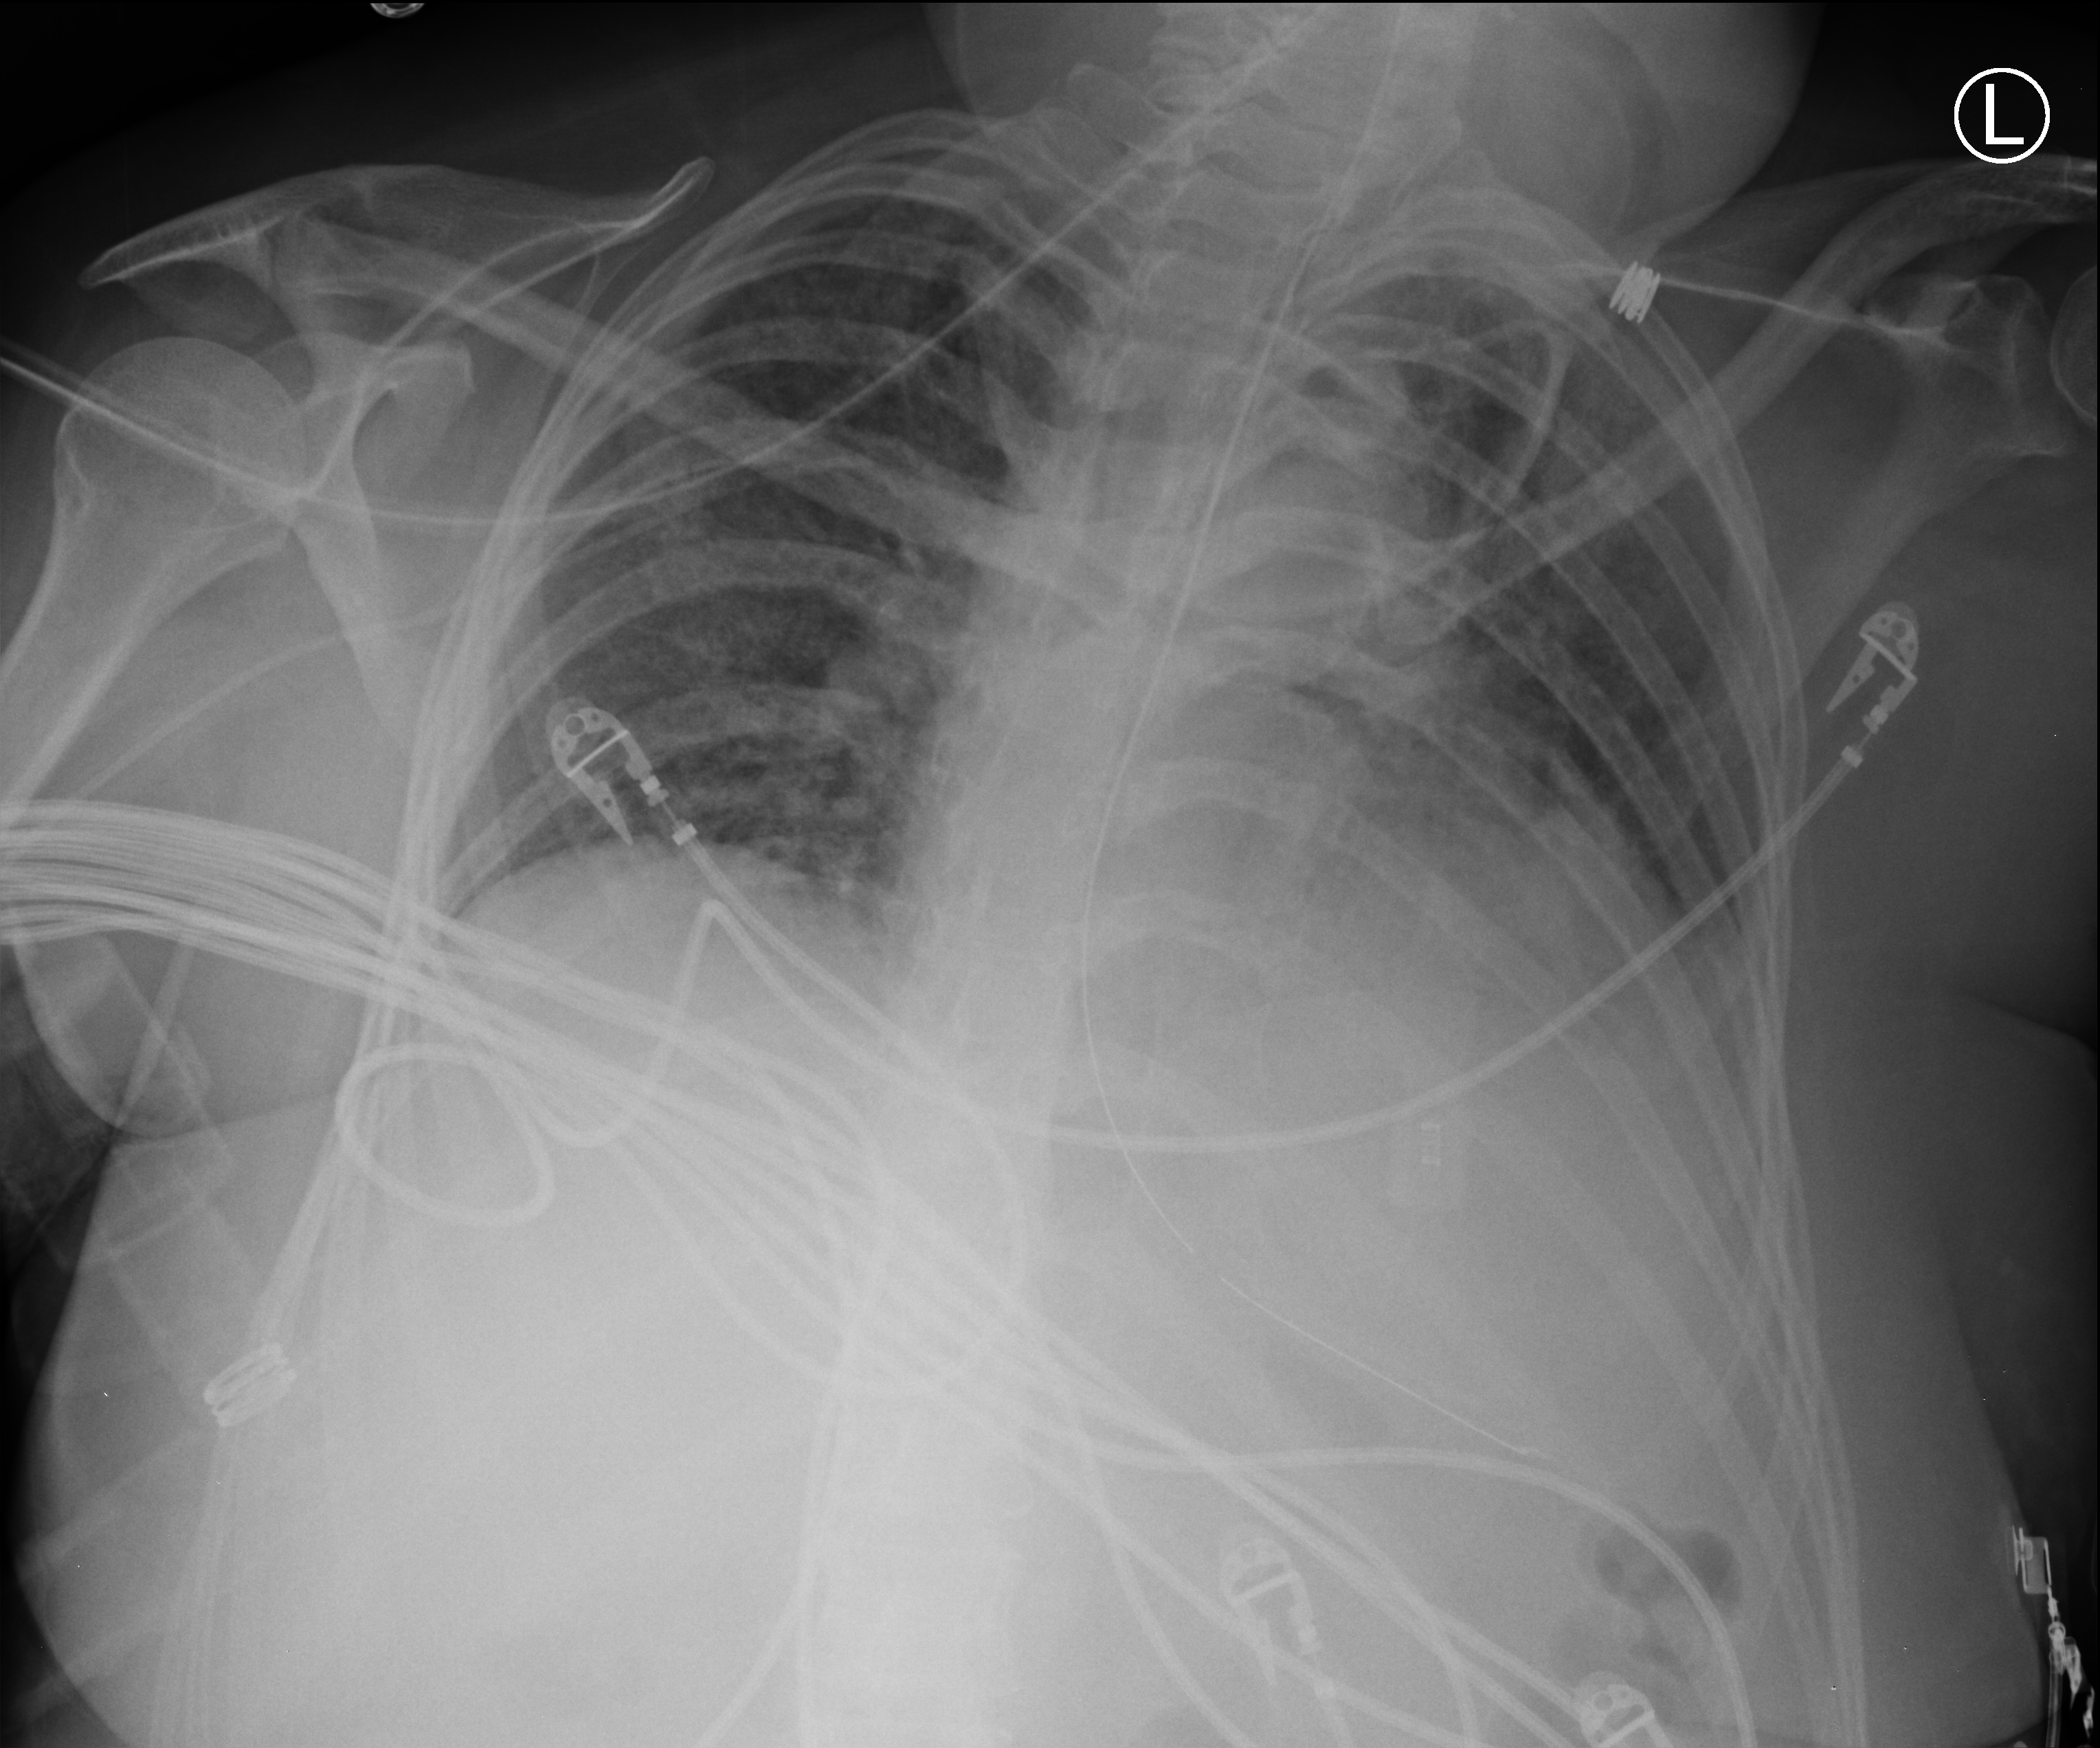
Bedside chest radiograph (computed radiography), anteroposterior (AP) projection. Female patient hospitalised with COVID-19, age 18–59 years.
Hospital-stay facts (about this admission, not read from this image; timing relative to this image not recorded): admitted to intensive care during this hospital stay: yes; smoking status (admission record): former; length of hospital stay: 73 days.